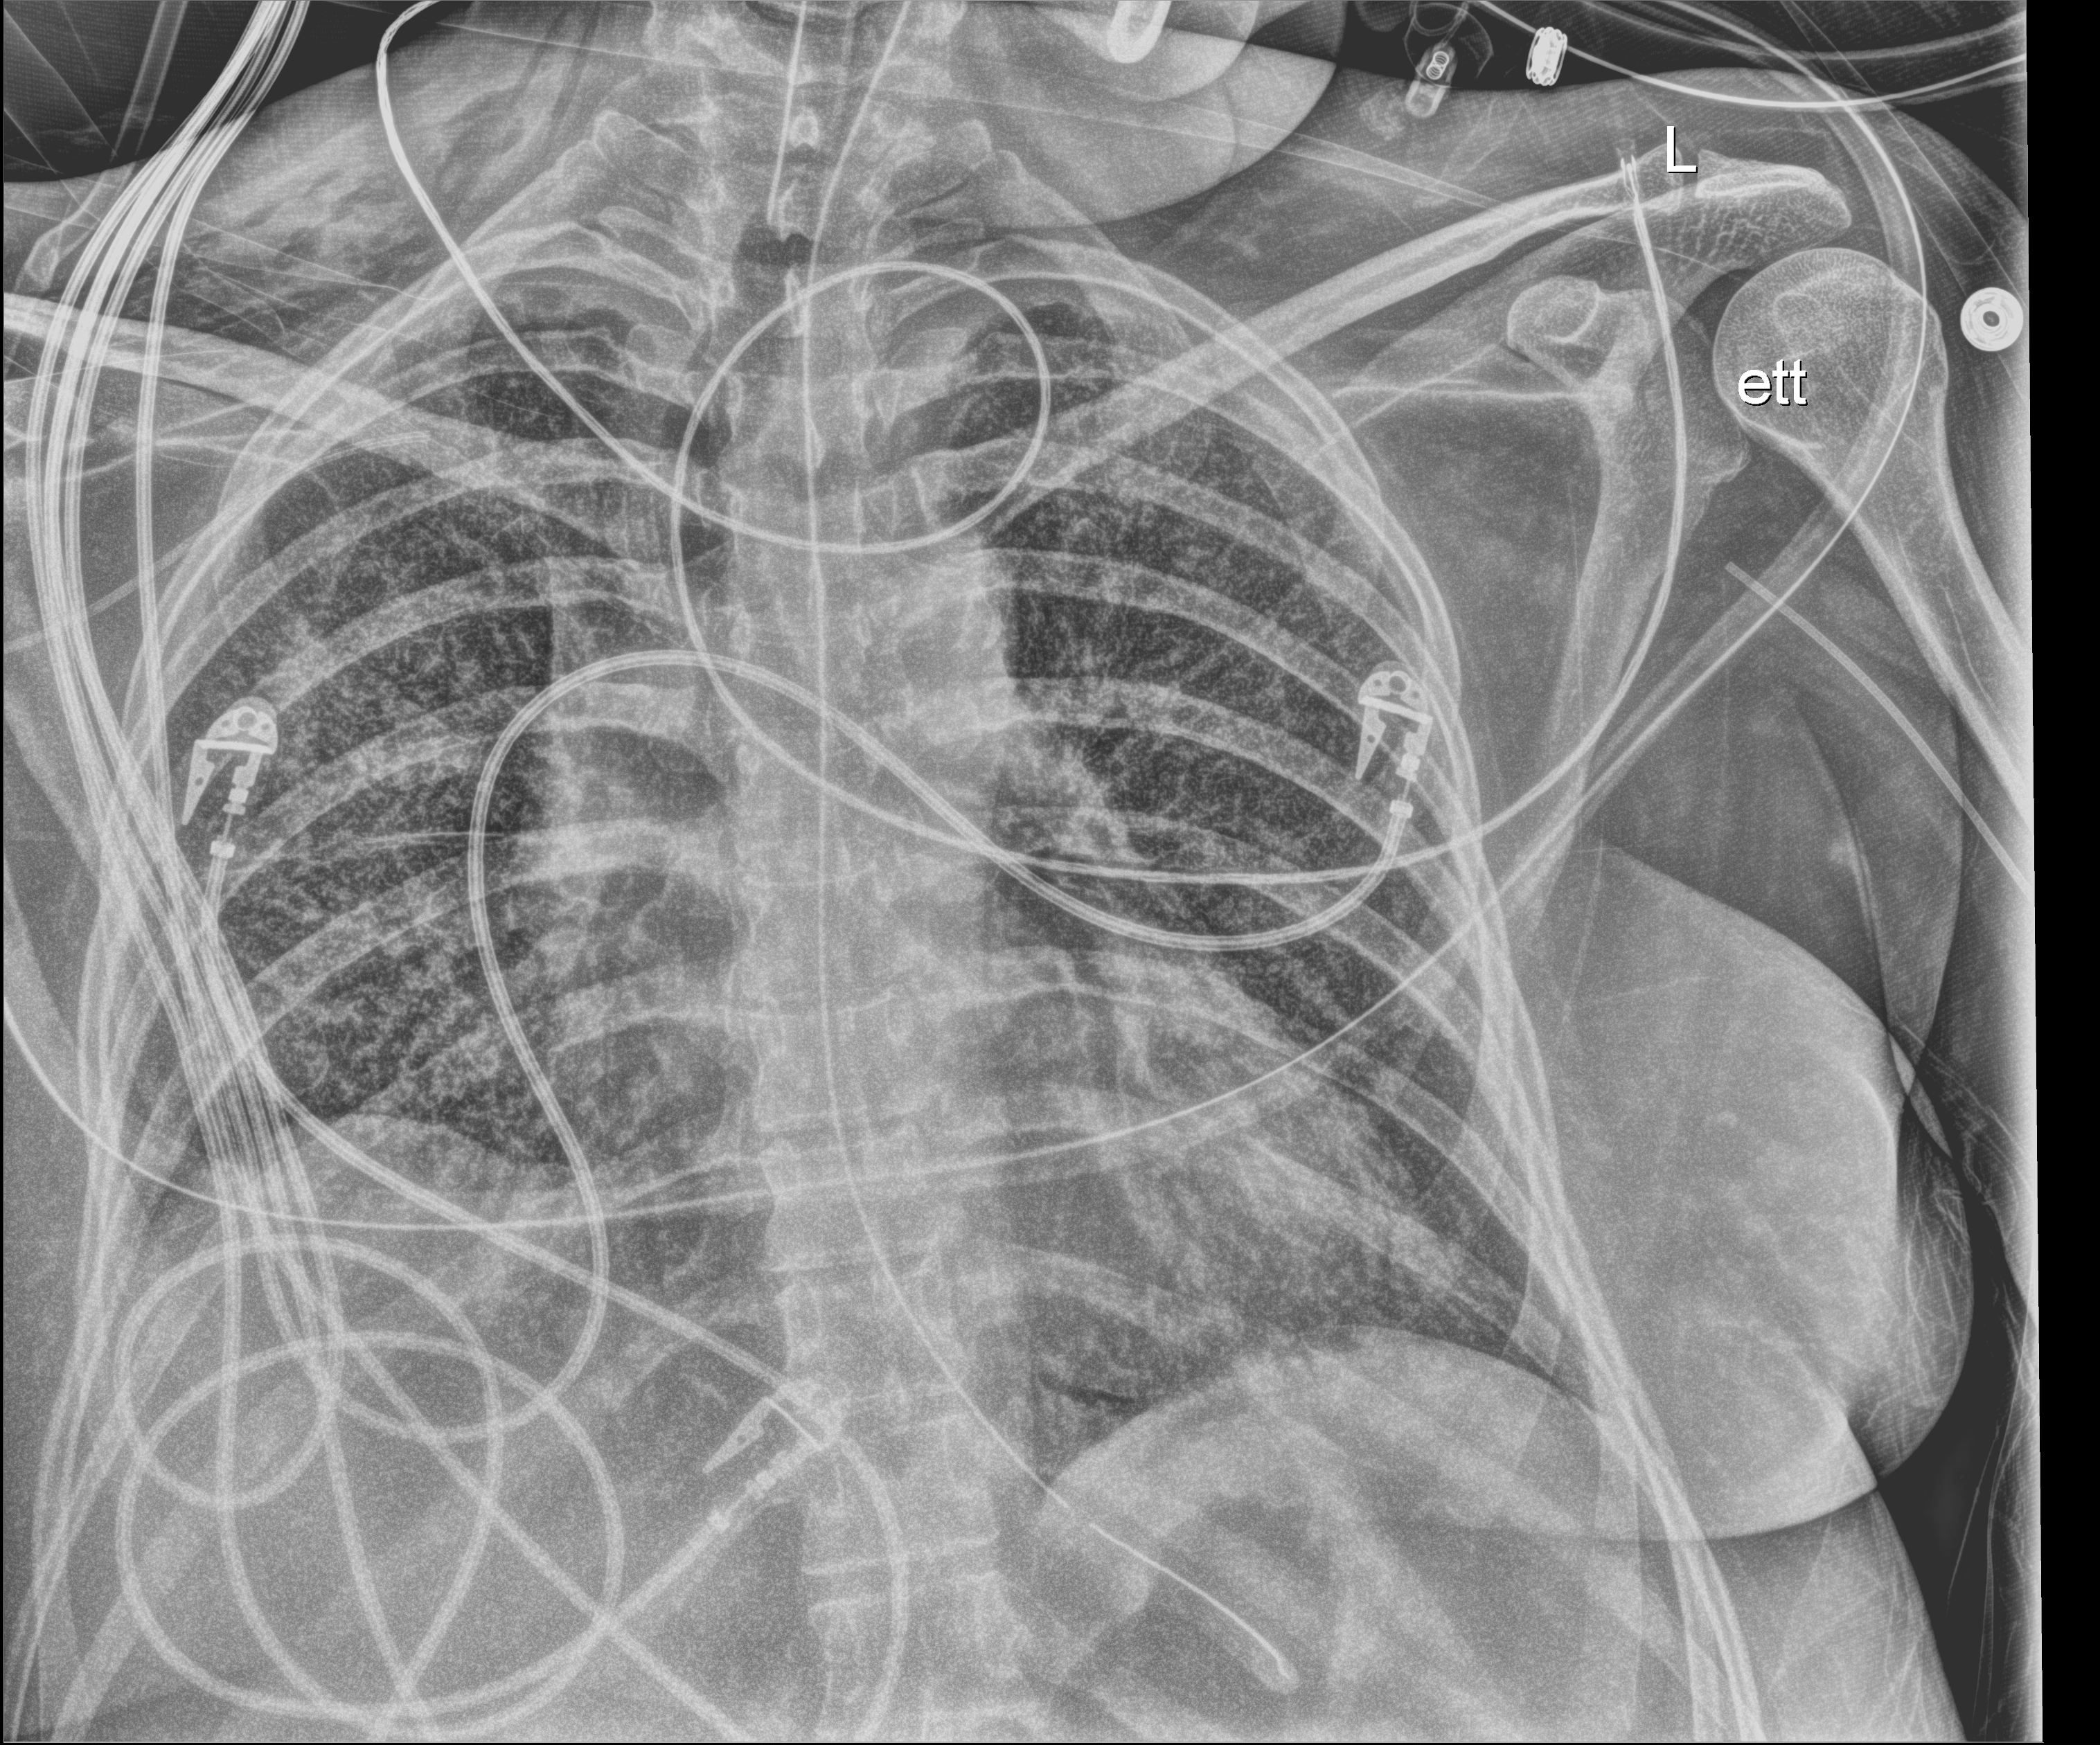
Chest X-ray (portable), anteroposterior (AP) projection. Female patient hospitalised with COVID-19, age 18–59 years.
From the hospital-stay record, not from the radiograph (when in the stay this image was taken is not recorded): mechanically ventilated during this hospital stay: yes; length of hospital stay: 73 days.